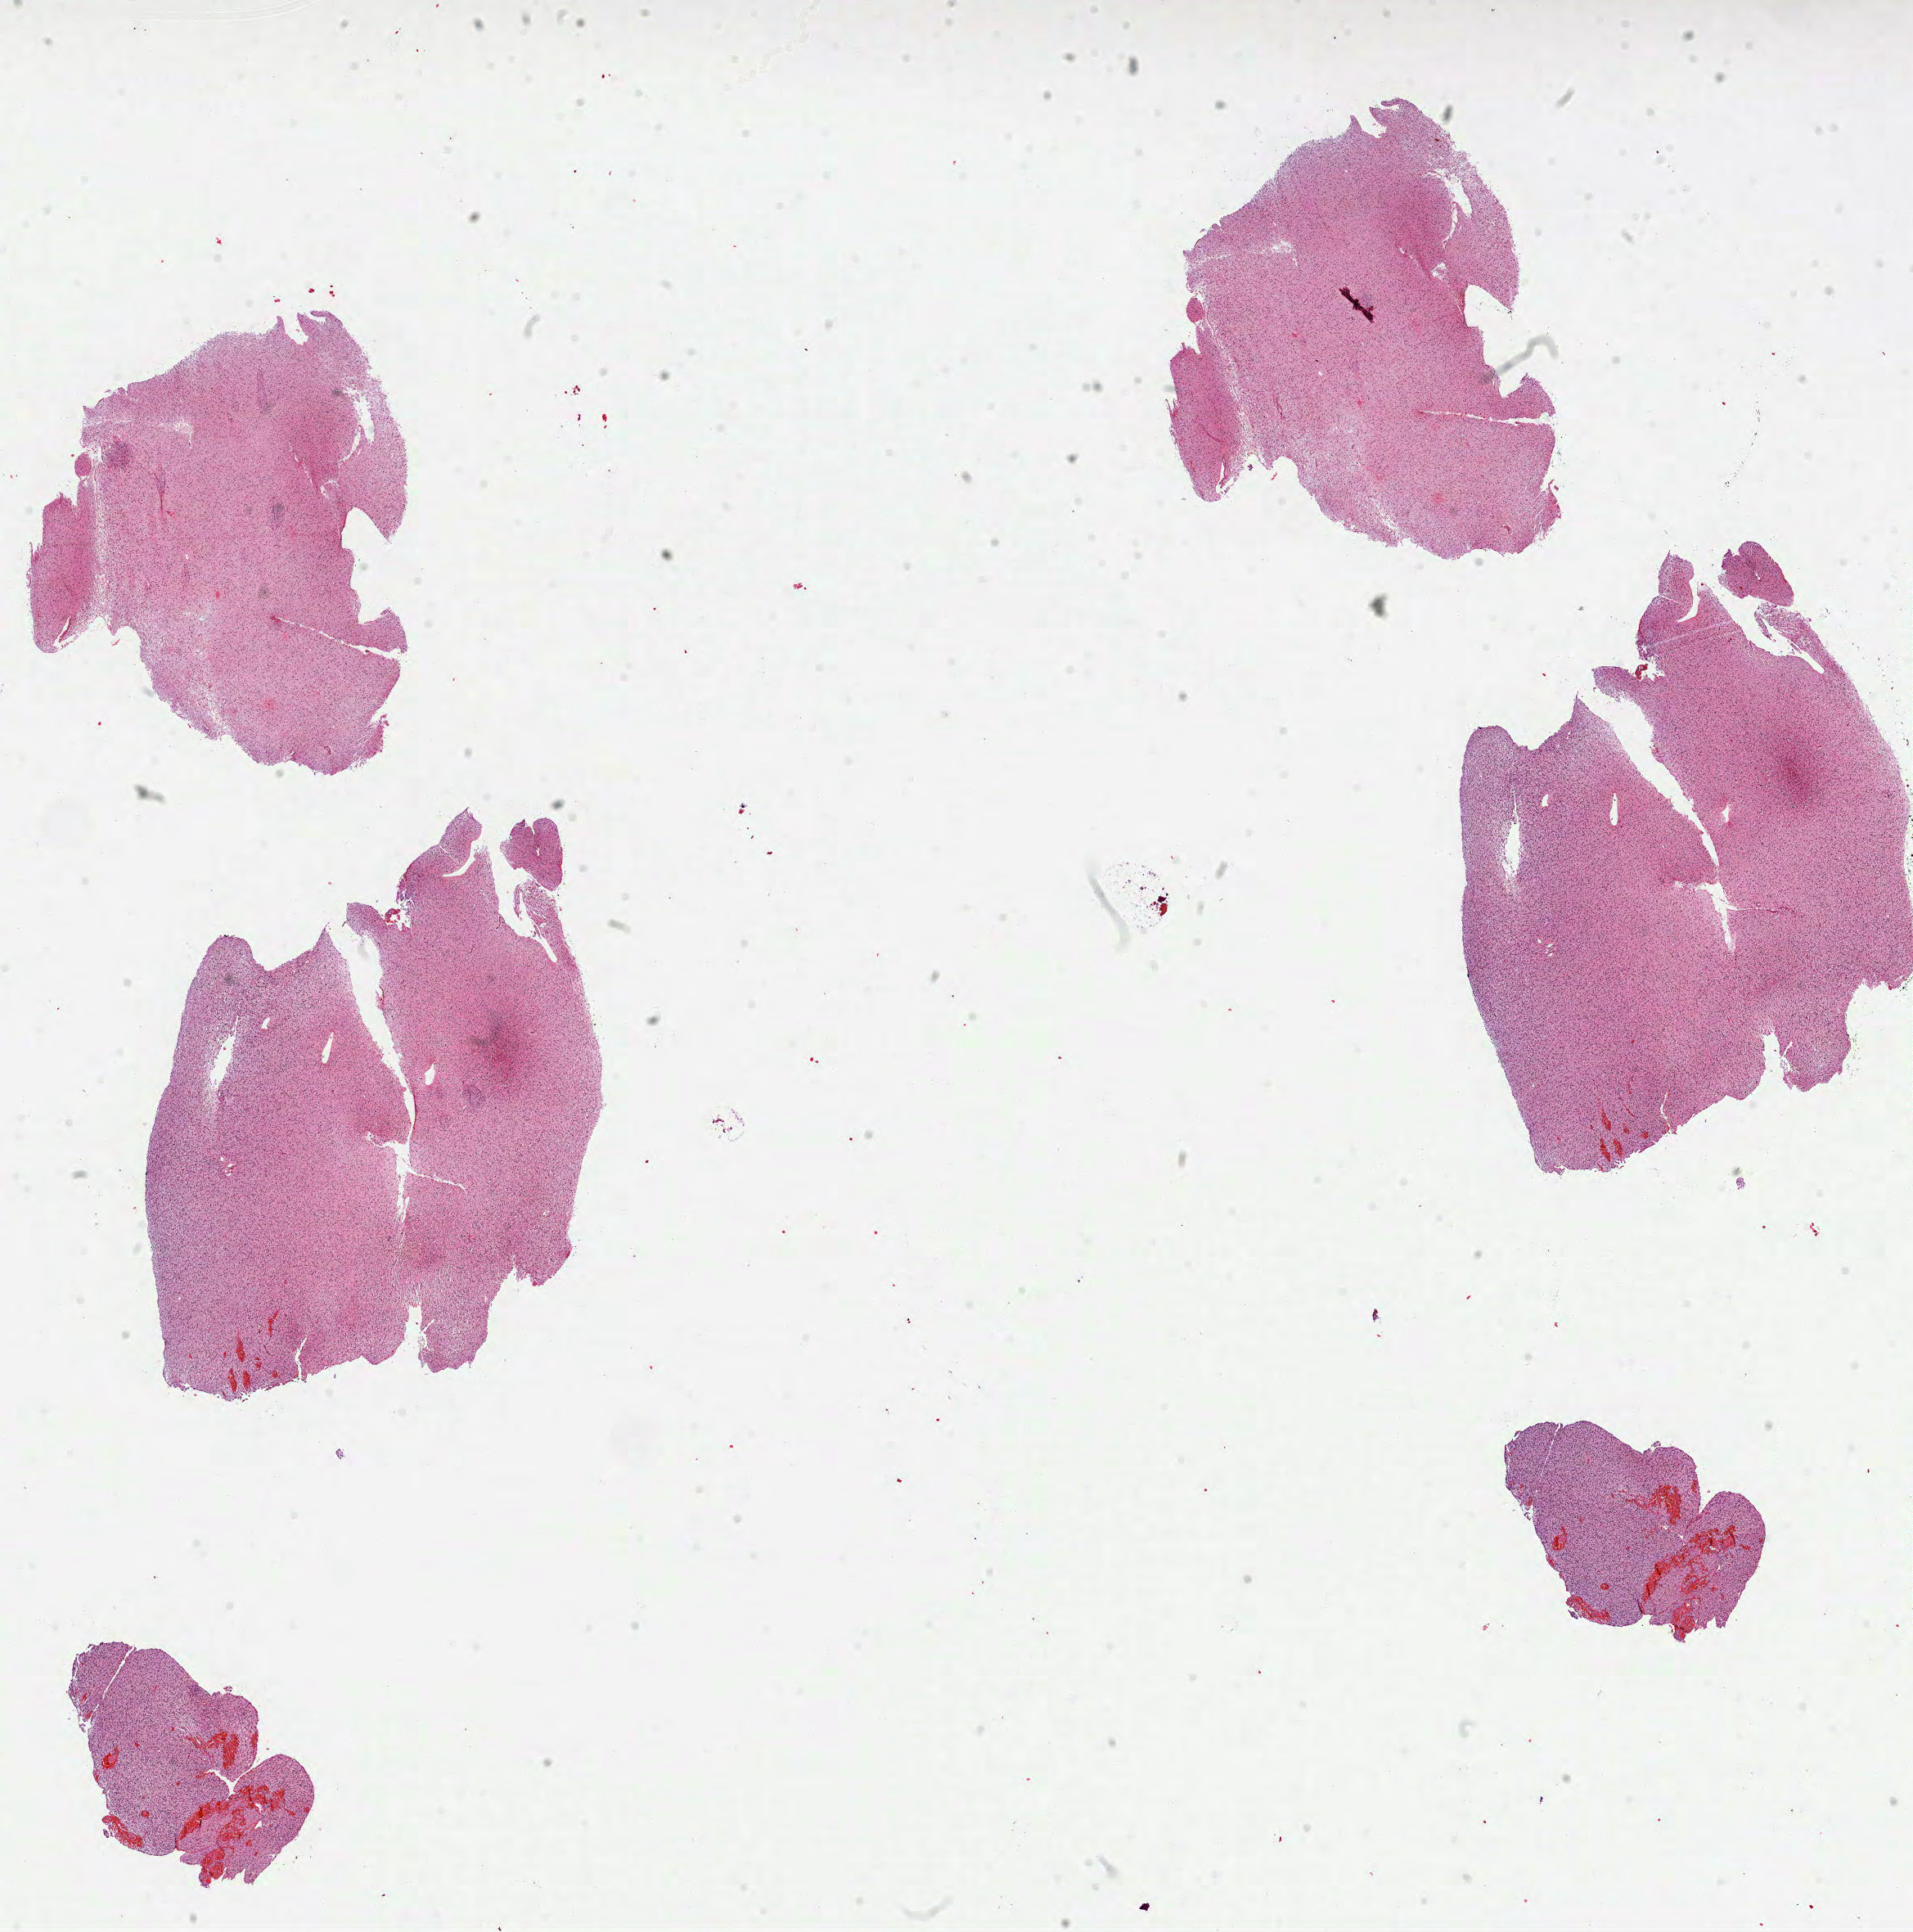
Whole-slide histology image, Hematoxylin and eosin (H&E) stained — whole scanned area (about 18.9 x 19.0 mm) shown as a low-resolution overview; formalin-fixed paraffin-embedded (FFPE) diagnostic section; sample: primary tumour, brain. Female, age 31 years at initial diagnosis. Histologic grade: G2 (moderately differentiated).
Pathologic diagnosis: Astrocytoma, NOS. Laterality: right.